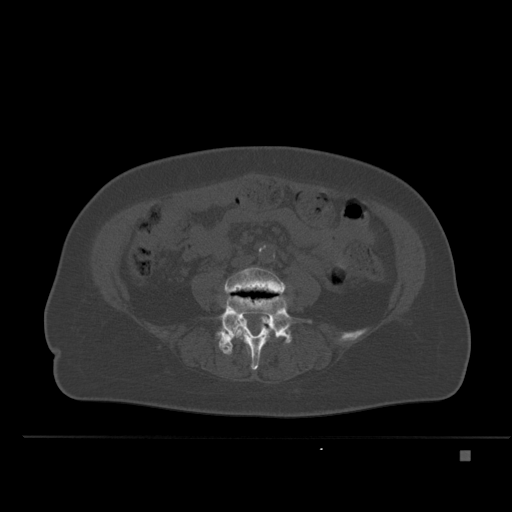
CT including the spine, one axial slice. Slice 168 of 477 in the series (ordered by position). Bone window (W 1800 / L 400 HU). 1.5 mm slice thickness. 512 × 512 image matrix, field of view 422 × 422 mm. Patient: female, 74 years. From the clinical record (not read from this slice): primary cancer: colon.
Outlined on this slice (semi-automatic segmentation, software-assisted and operator-edited):
- L4 vertebra: bounding box (x1, y1, x2, y2) in pixels: (223, 267, 287, 338)
- L5 vertebra: (218, 293, 292, 370)